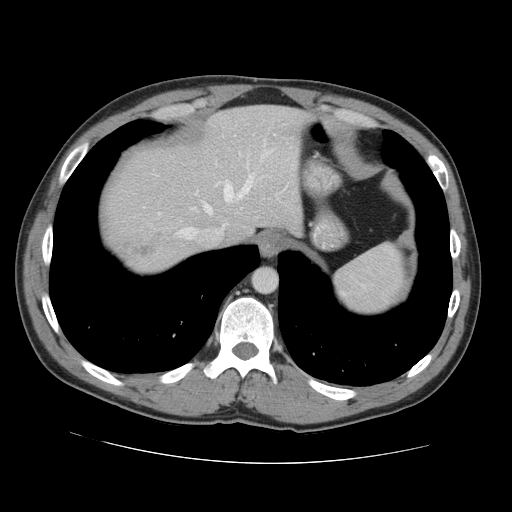
Contrast-enhanced abdominal CT, one axial slice; position 118 of 131 along the scan axis; 120 kVp; intravenous contrast given; soft-tissue window (W 400 / L 40 HU); 512 × 512 image matrix, field of view 380 × 380 mm. Male patient, age 40 years. From the clinical record (not read from this slice): diagnosis: colorectal cancer liver metastases, imaged before liver resection; multiple liver metastases: yes; largest metastasis: 2.9 cm; disease in both lobes: yes.
Structures marked on this image (expert manual segmentation):
- hepatic veins: bounding box [x1, y1, x2, y2] px = [179, 176, 252, 238]
- liver: [102, 106, 307, 272]
- planned liver remnant (the part of the liver to remain after resection): [124, 106, 307, 241]
- liver metastasis: [127, 243, 151, 259]